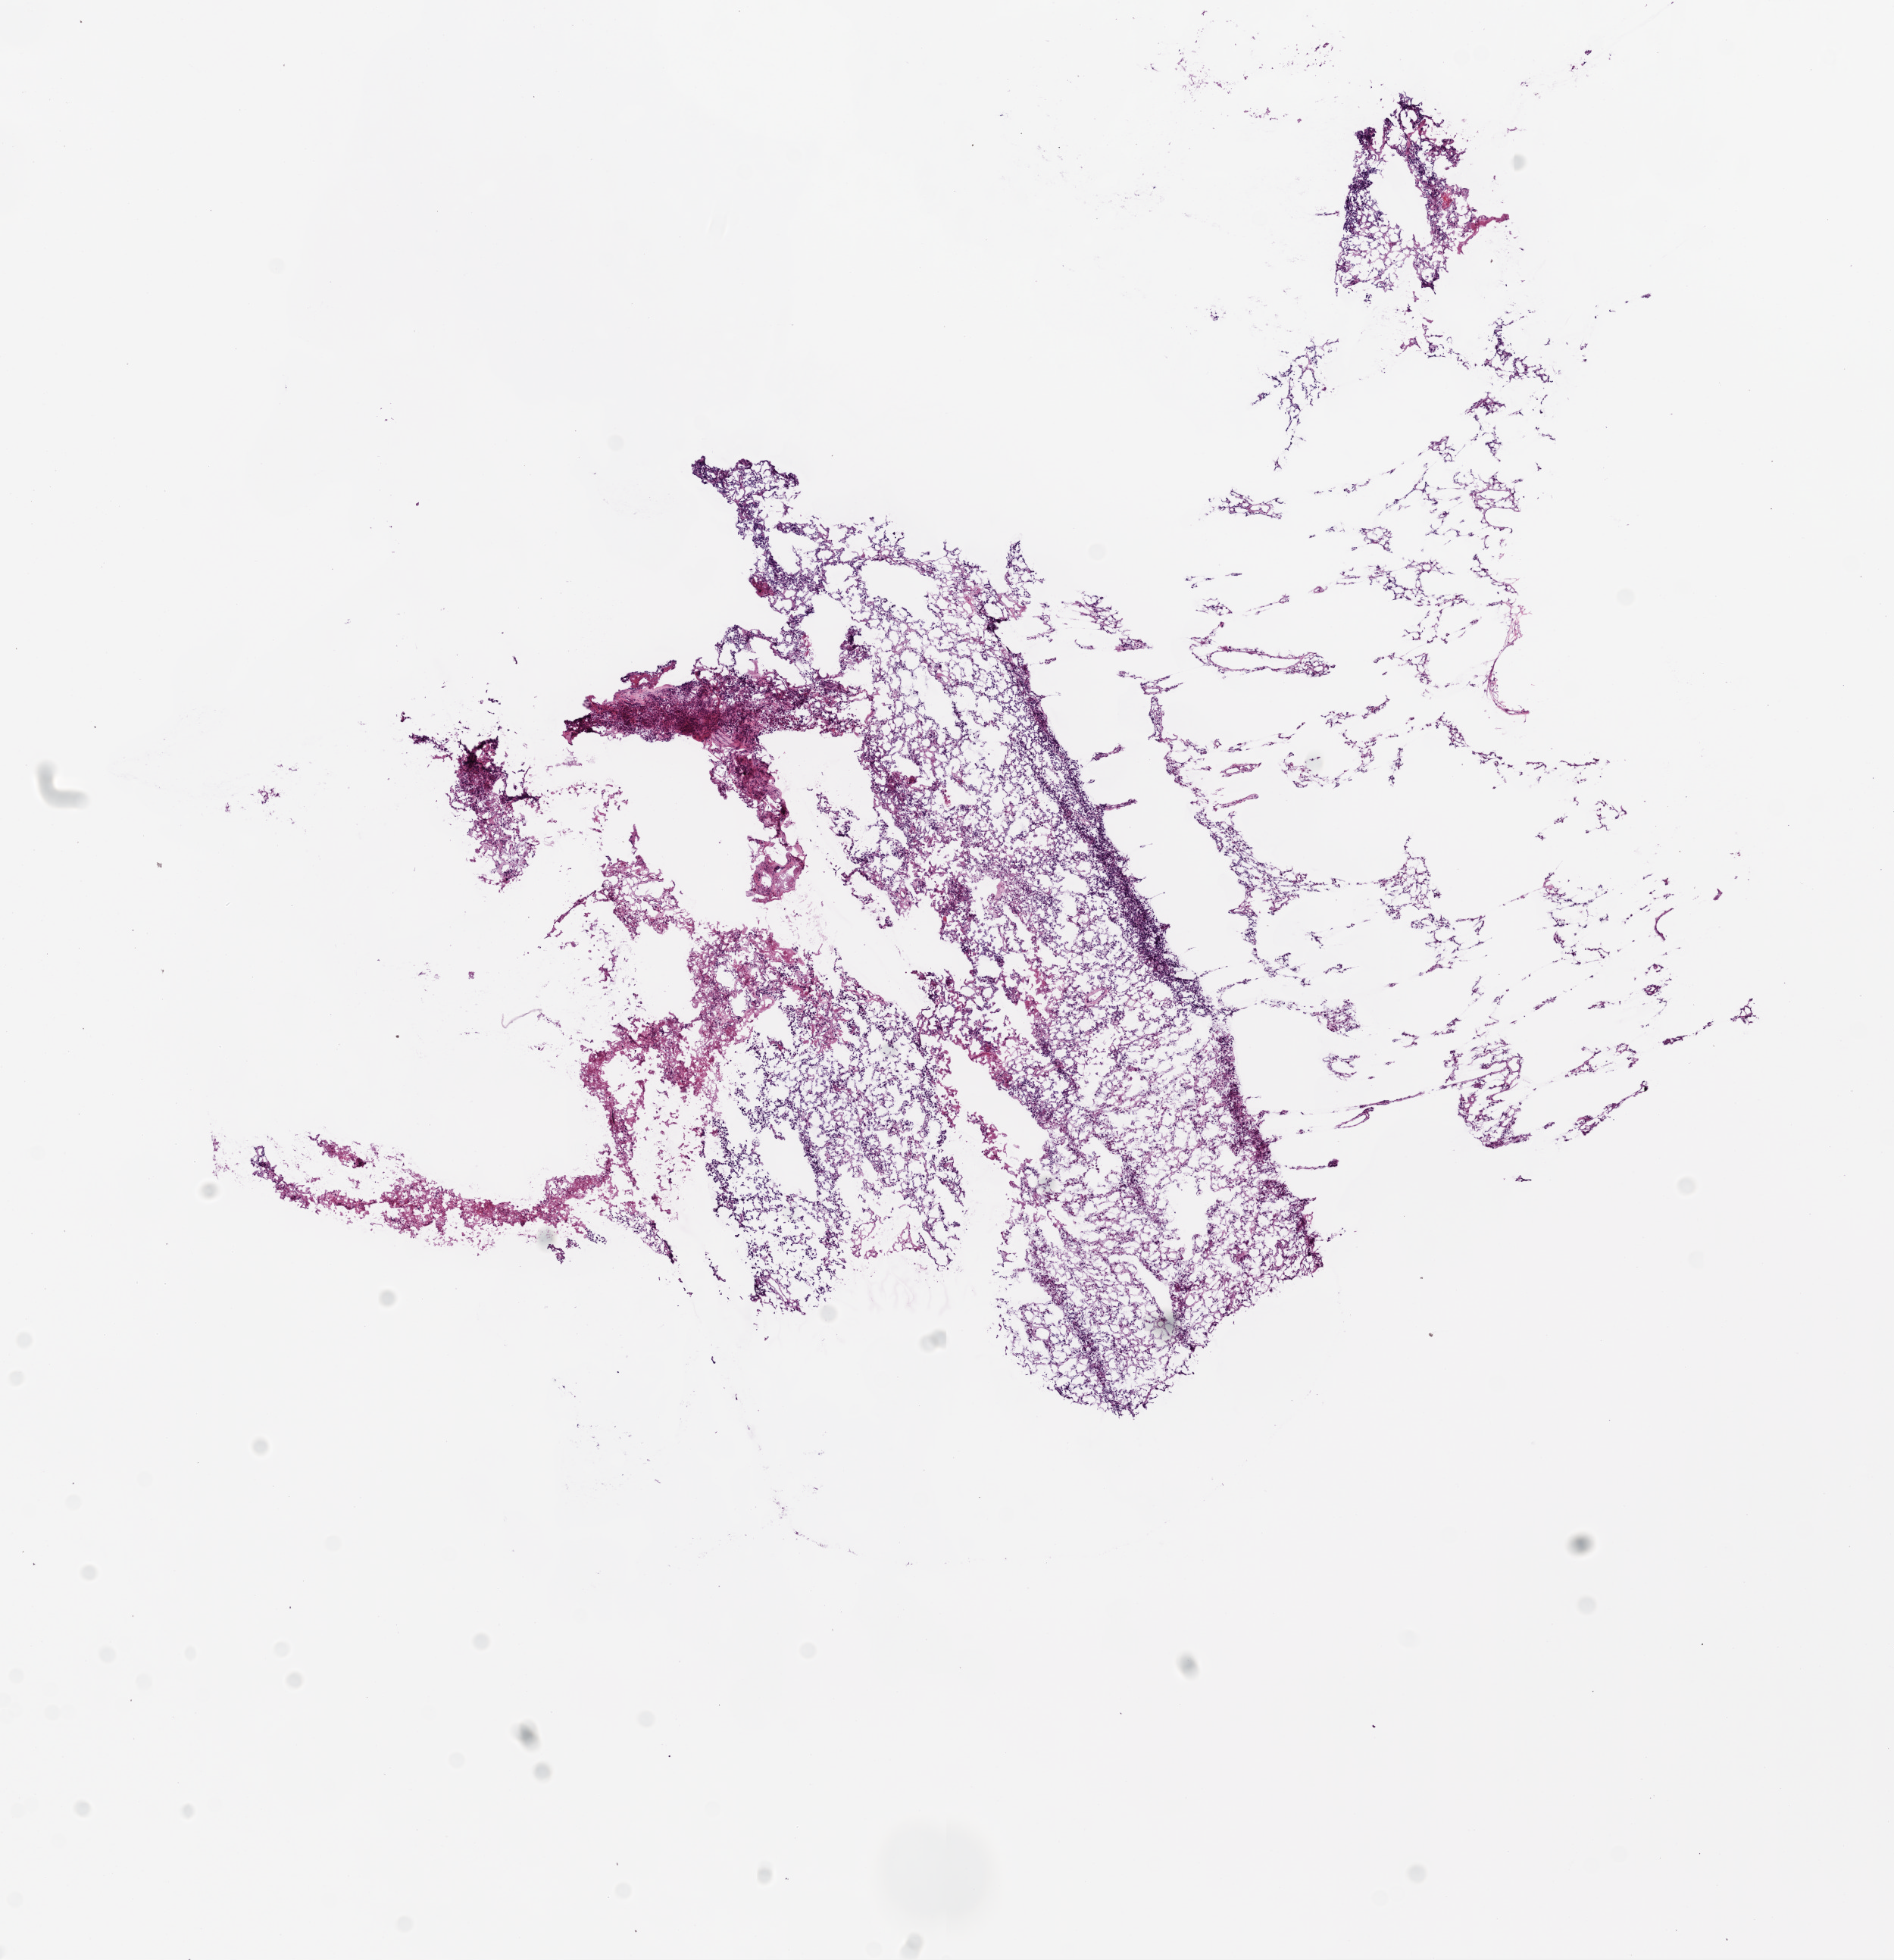
Digitized H&E-stained tissue section (whole slide) — low-resolution overview of the scanned area, about 10.0 x 10.4 mm (slide scanned at 20x); frozen section from the top of the tissue portion; sample: primary tumour, brain. Male patient; age at initial diagnosis 70 years. Slide review estimates, as recorded: tumour cells 80%, tumour nuclei 80%, normal cells 0%, stromal cells 0%, necrosis 20%.
• diagnosis: Glioblastoma